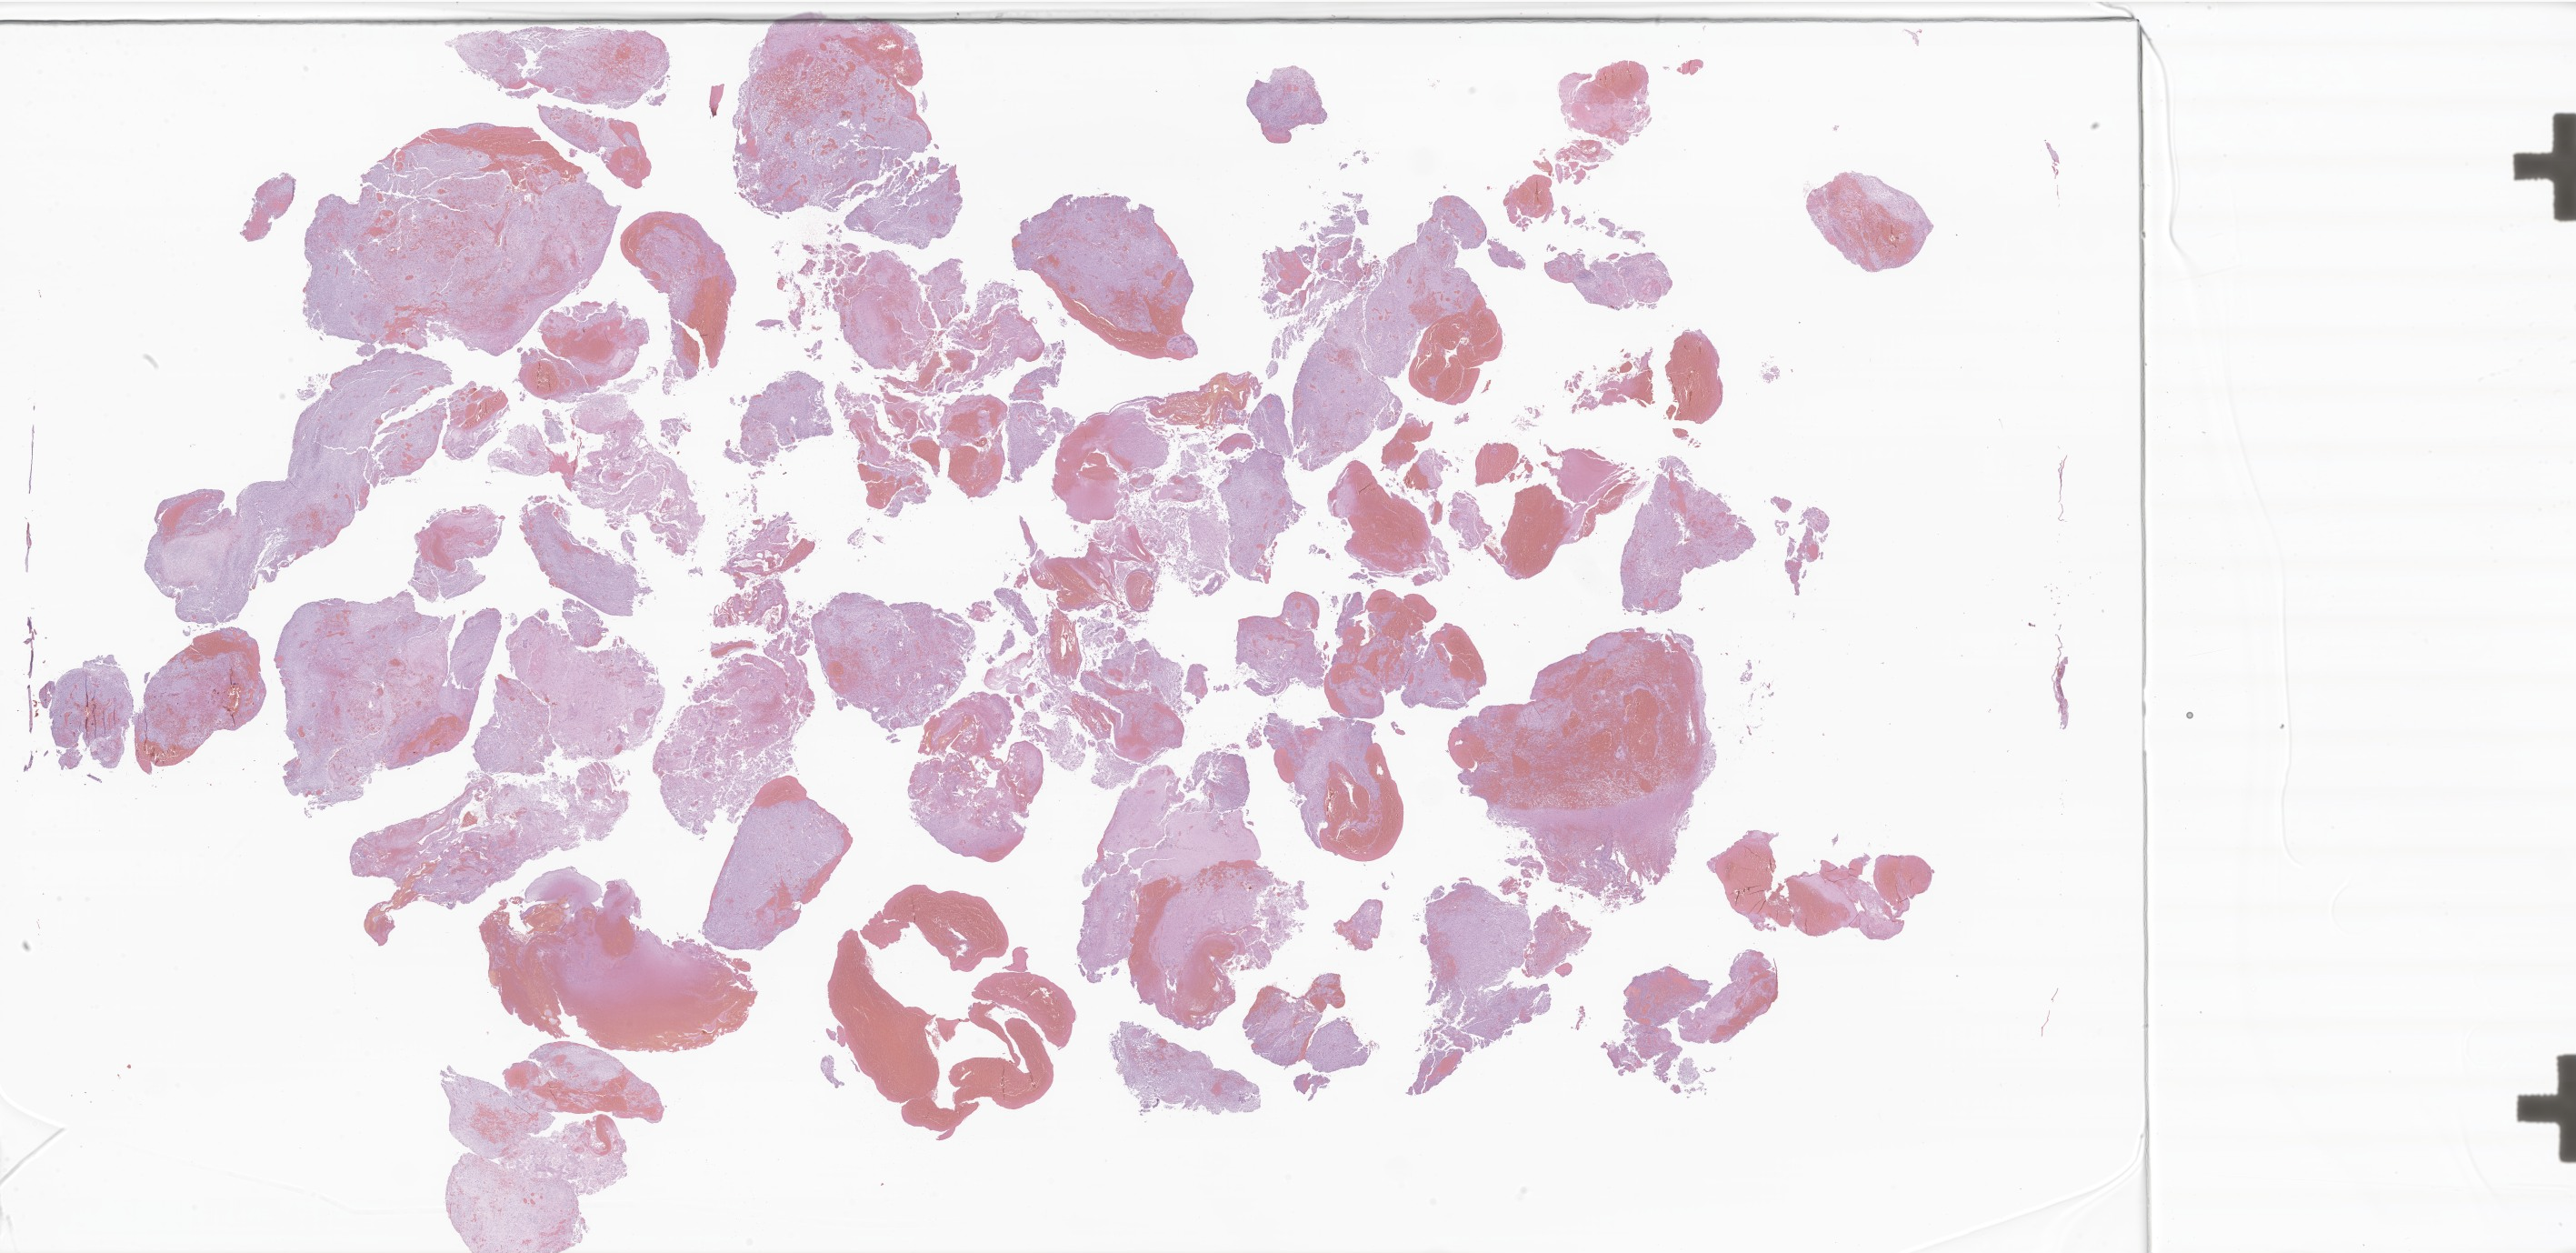
H&E whole-slide image of tumor tissue from the cerebral ventricle — low-resolution overview of the scanned area, about 47.8 x 23.2 mm. Formalin-fixed, paraffin-embedded (FFPE) tissue. Patient: male, age 83 months (6 years 11 months).
* recorded diagnosis: Subependymal giant cell astrocytoma